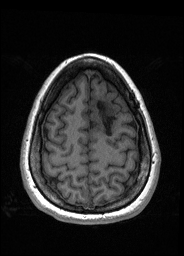
Pre-operative brain MRI before brain-tumour surgery, one axial slice. Position 48 of 176 along the scan axis. T1-weighted post-contrast. 1 mm slice thickness. 184 × 256 image matrix. Case-level facts recorded for this patient, not image findings: histopathology: Oligodendroglioma; WHO grade: 2; IDH mutation: yes; tumour location: Left Frontal.
Structures marked on this image (outlined manually by an expert reader):
- tumour: box from (x=91, y=103) to (x=117, y=134) px